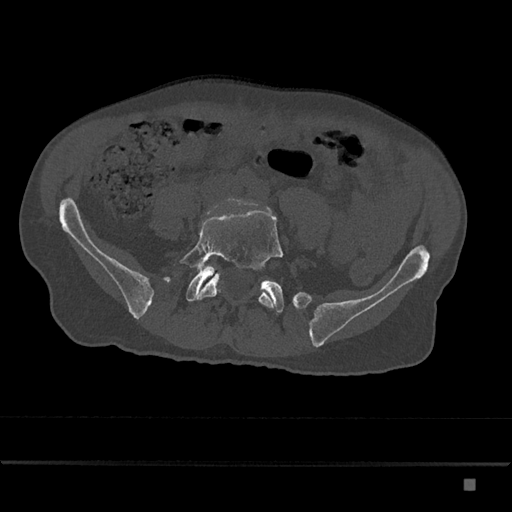
CT including the spine, one axial slice. Position 268 of 797 along the scan axis. Bone window (W 1800 / L 400 HU). 0.5 mm slice thickness. 512 × 512 image matrix, field of view 390 × 390 mm. Male patient, age 72 years. Case-level facts recorded for this patient, not image findings: primary cancer: prostate.
Annotated regions visible in this slice (semi-automatic segmentation, software-assisted and operator-edited):
- L5 vertebra: box from (x=179, y=210) to (x=283, y=308) px